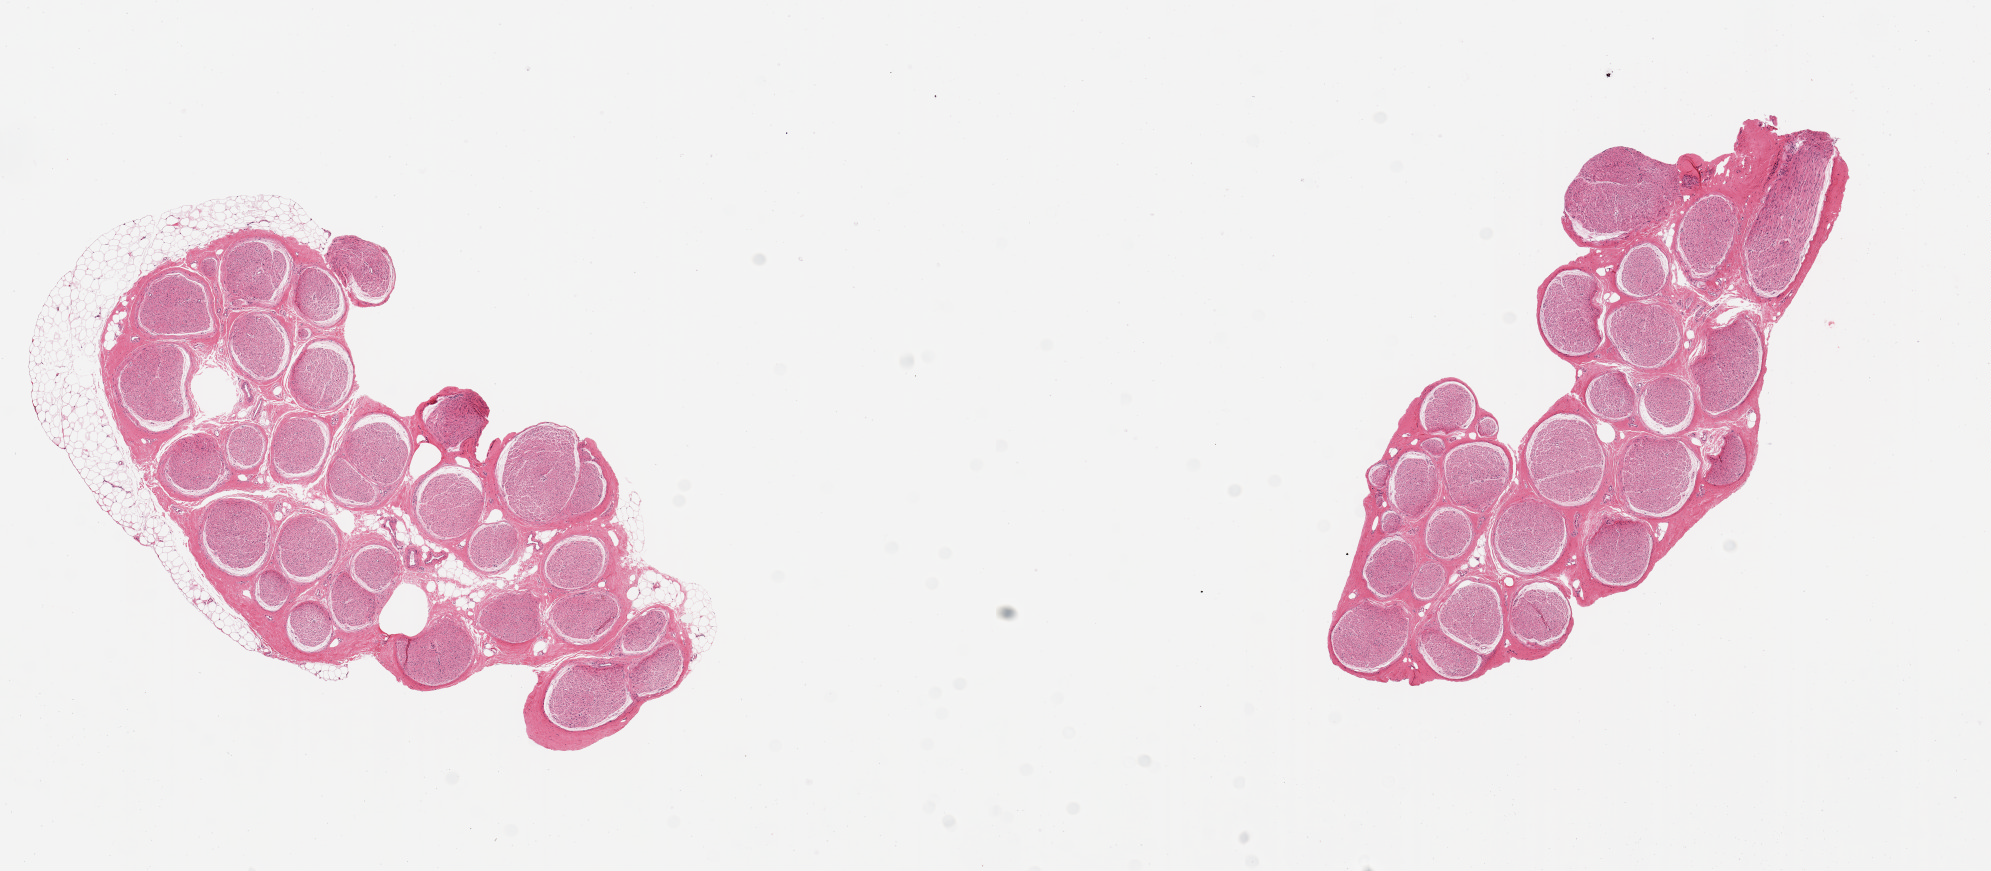
Digitized hematoxylin and eosin (H&E)-stained section, brightfield — a low-resolution overview of the entire scanned area, about 15.8 x 6.9 mm, PAXgene-fixed paraffin-embedded (PFPE) section, target tissue: tibial nerve, donor tissue sample. Donor: female.
Review note (as recorded): 2 pieces. 6x3 & 6x2mm; 10% external adipose in 1; none in other.